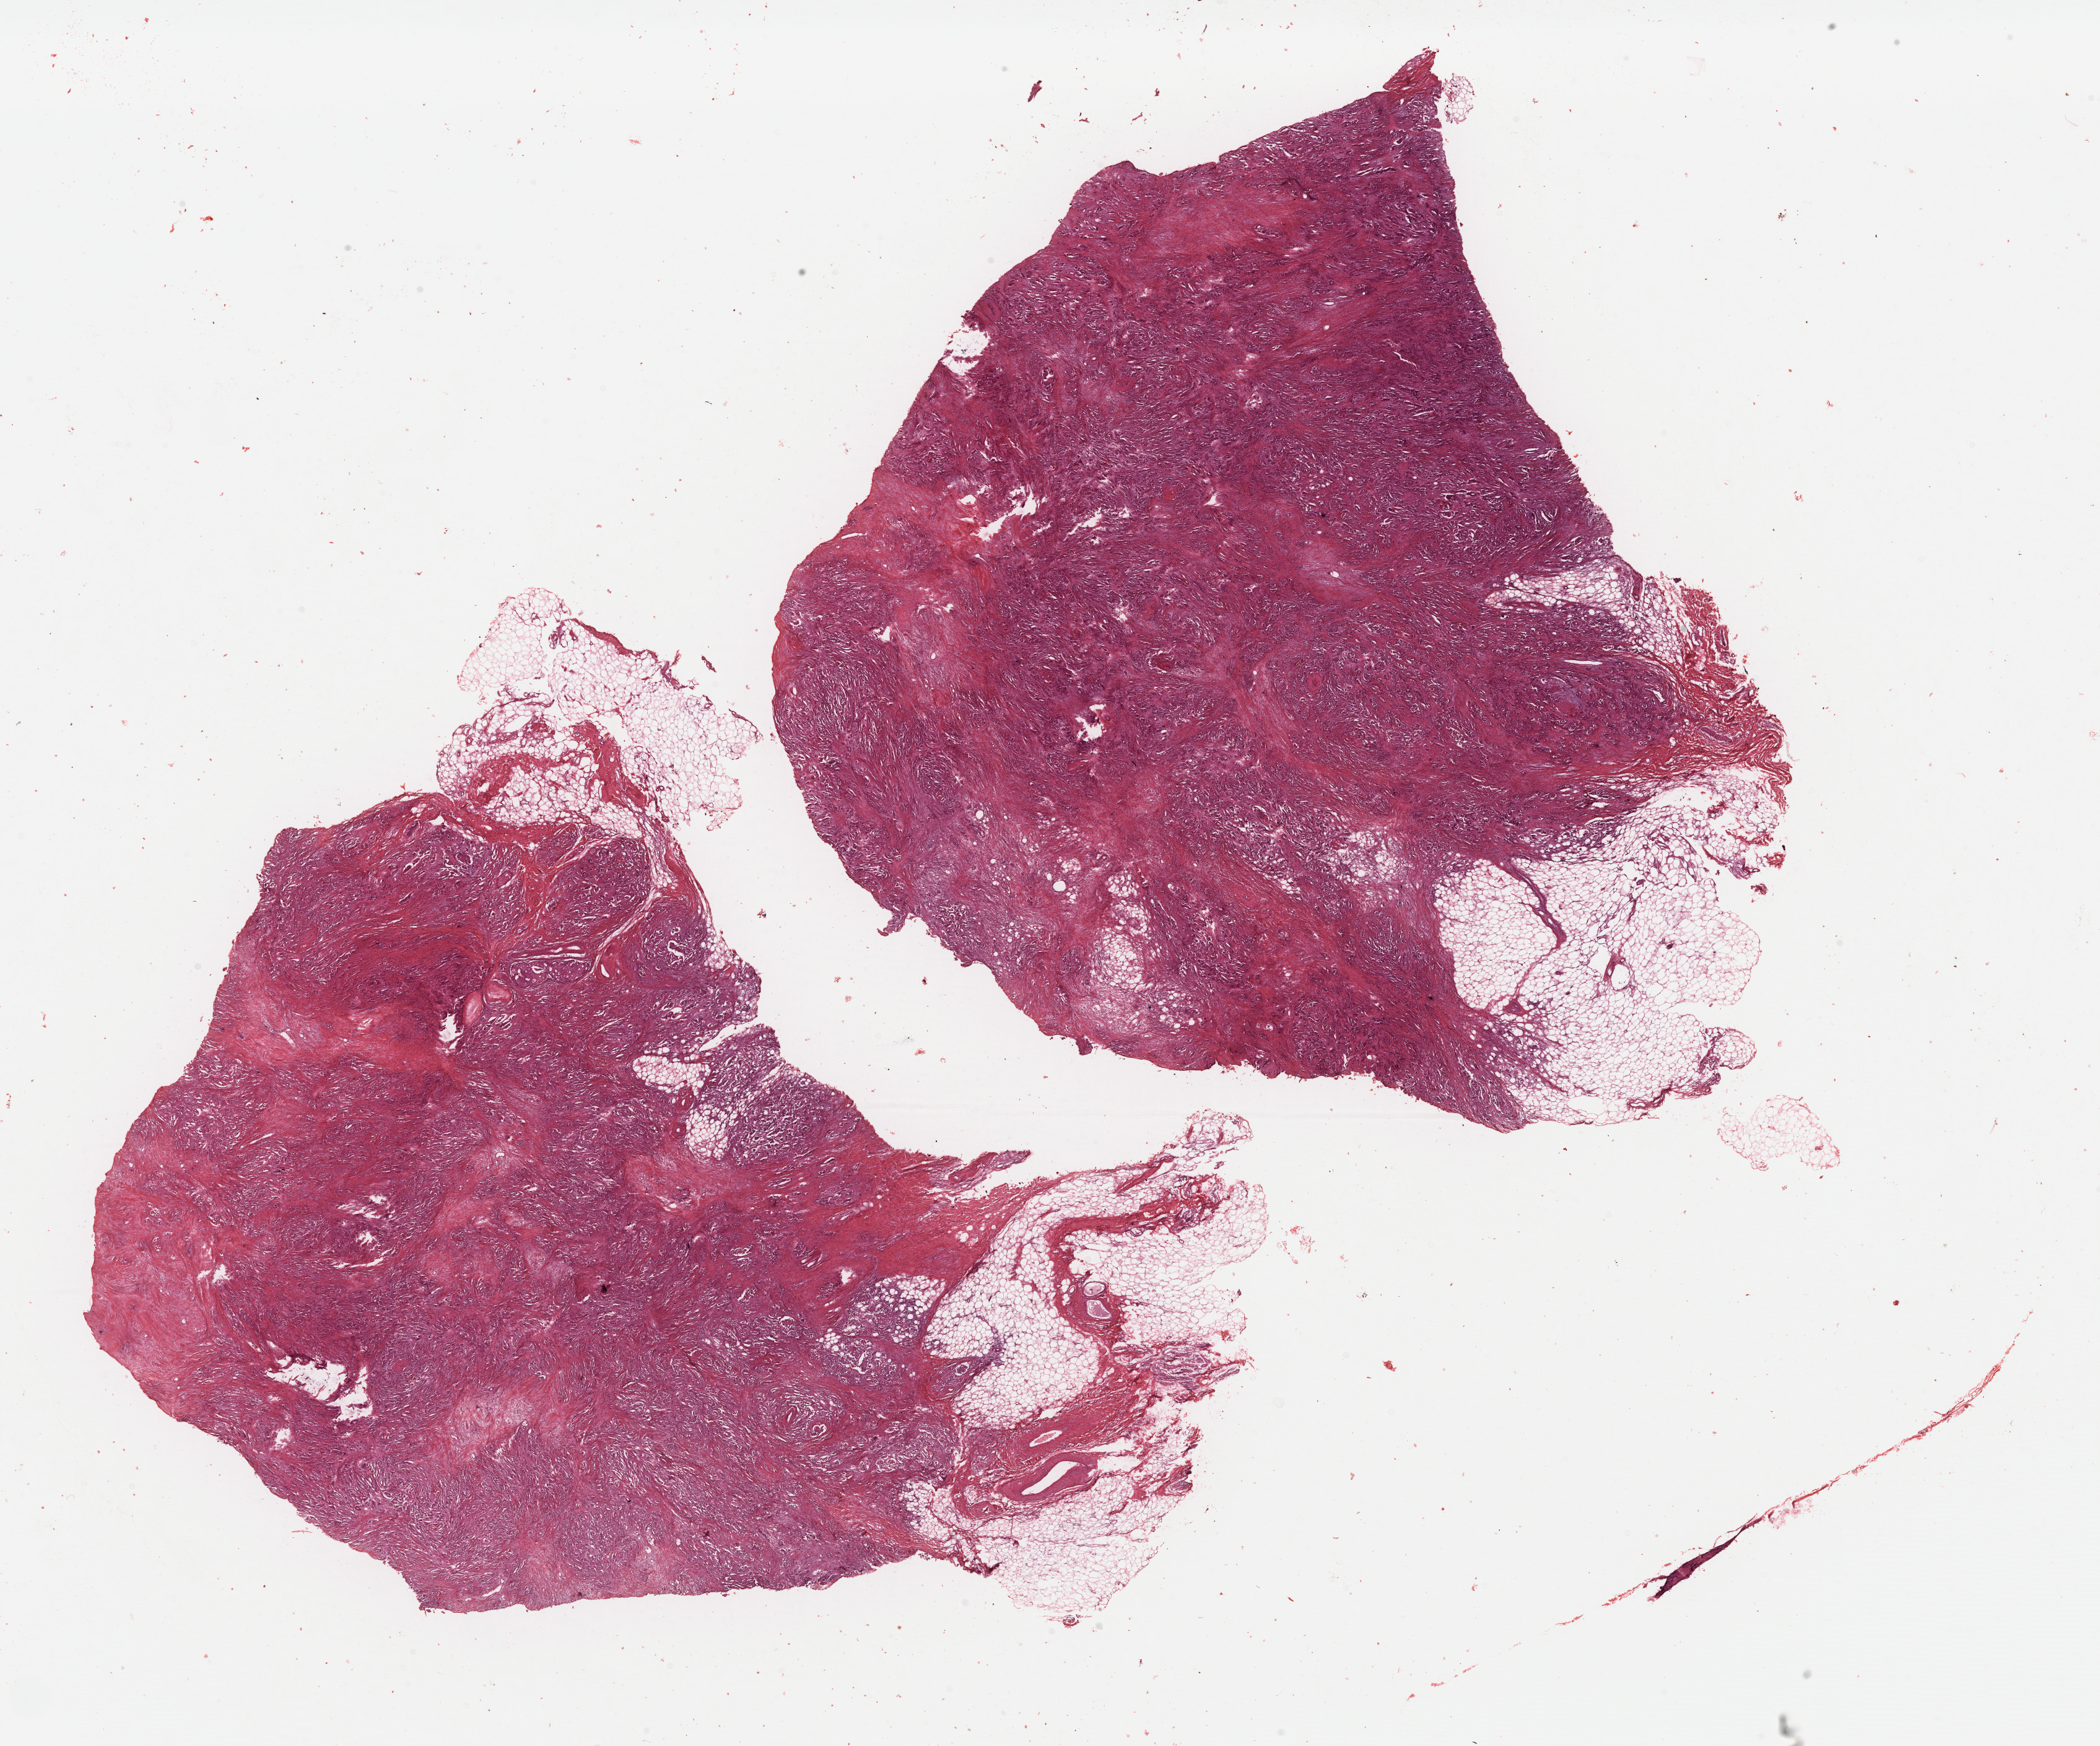
Whole-slide histology image, H&E — shown as a low-resolution overview of the whole scanned area (about 26.8 x 22.2 mm), FFPE section, primary tumour sample from the breast. Female, age 46 years at initial diagnosis.
• pathologic diagnosis: Lobular carcinoma, NOS
• AJCC pathologic stage: IIA (7th edition)
• TNM: T2 N0 M0
• lymph nodes positive (case pathology): 0 of 16 examined
• laterality: left